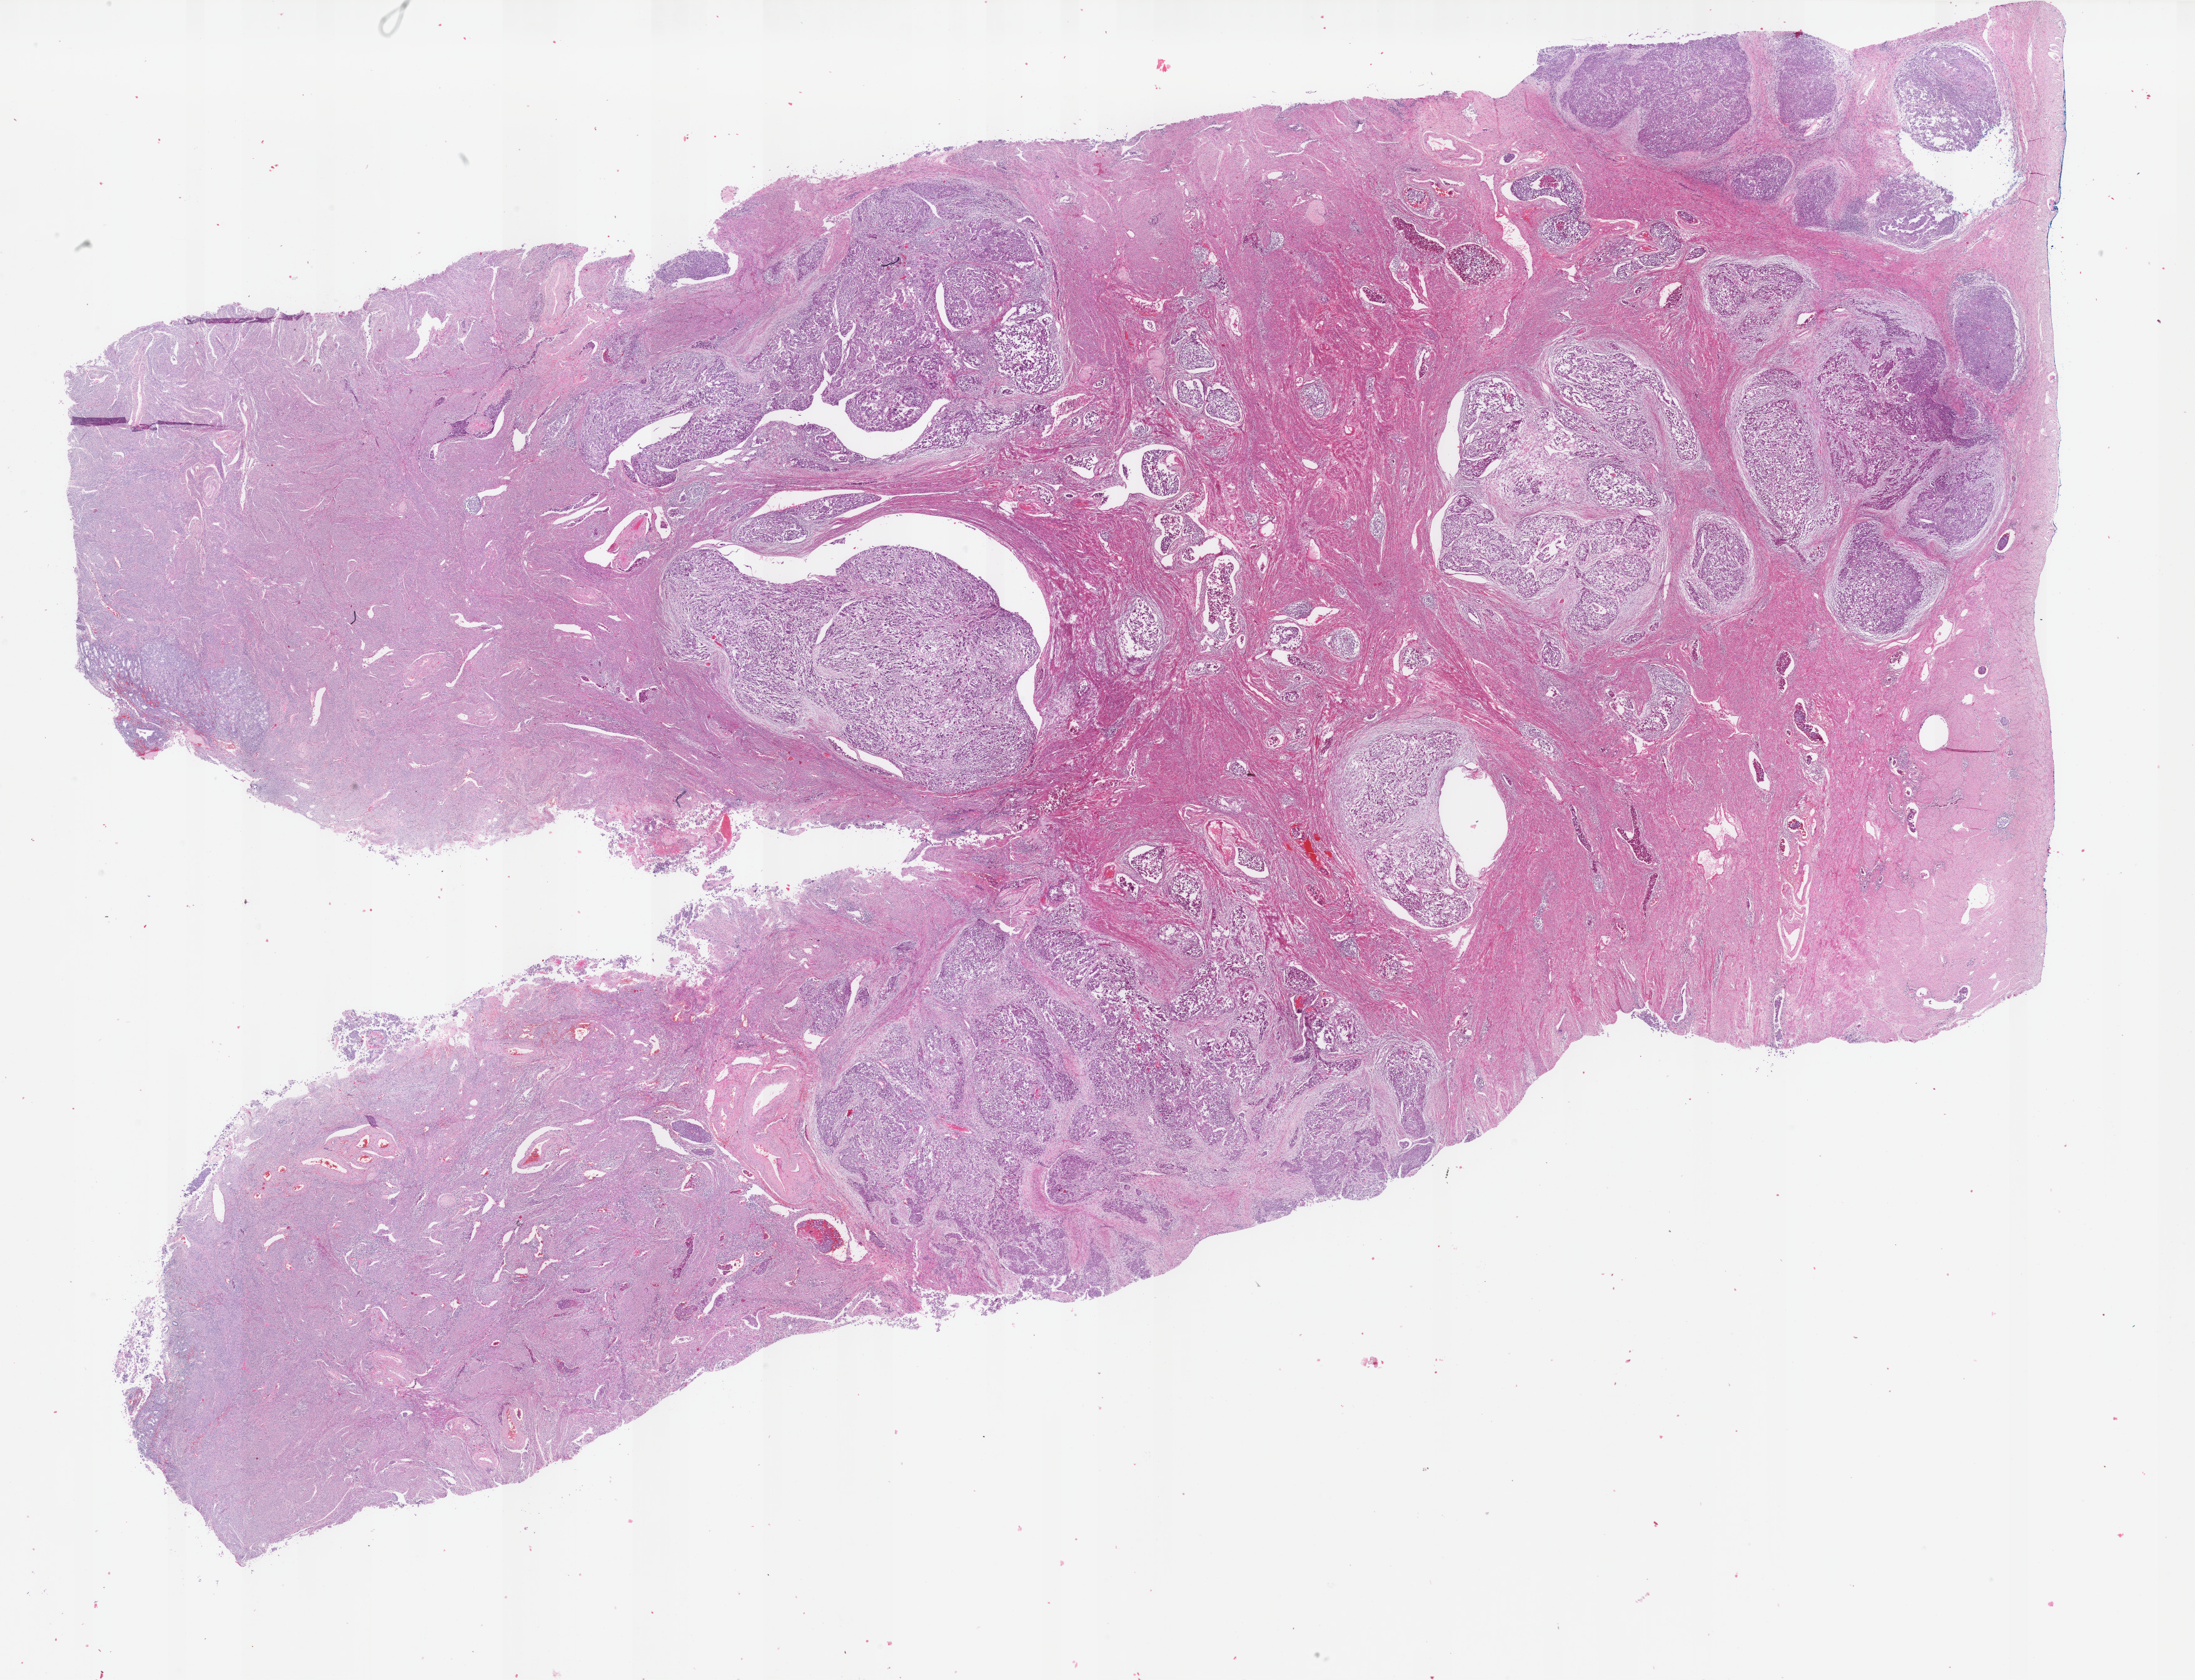
Whole-slide histology image, H&E, shown as a low-resolution overview of the whole scanned area (about 27.9 x 21.3 mm, slide scanned at 40x); formalin-fixed paraffin-embedded (FFPE) diagnostic section; primary tumour sample from the uterus. Patient: female, age at initial diagnosis 66 years. Histologic grade: G3 (poorly differentiated).
• FIGO stage: IIIC2
• lymph nodes positive (case pathology): 1 of 5 examined
• histologic diagnosis: Carcinoma, undifferentiated, NOS (endometrium)